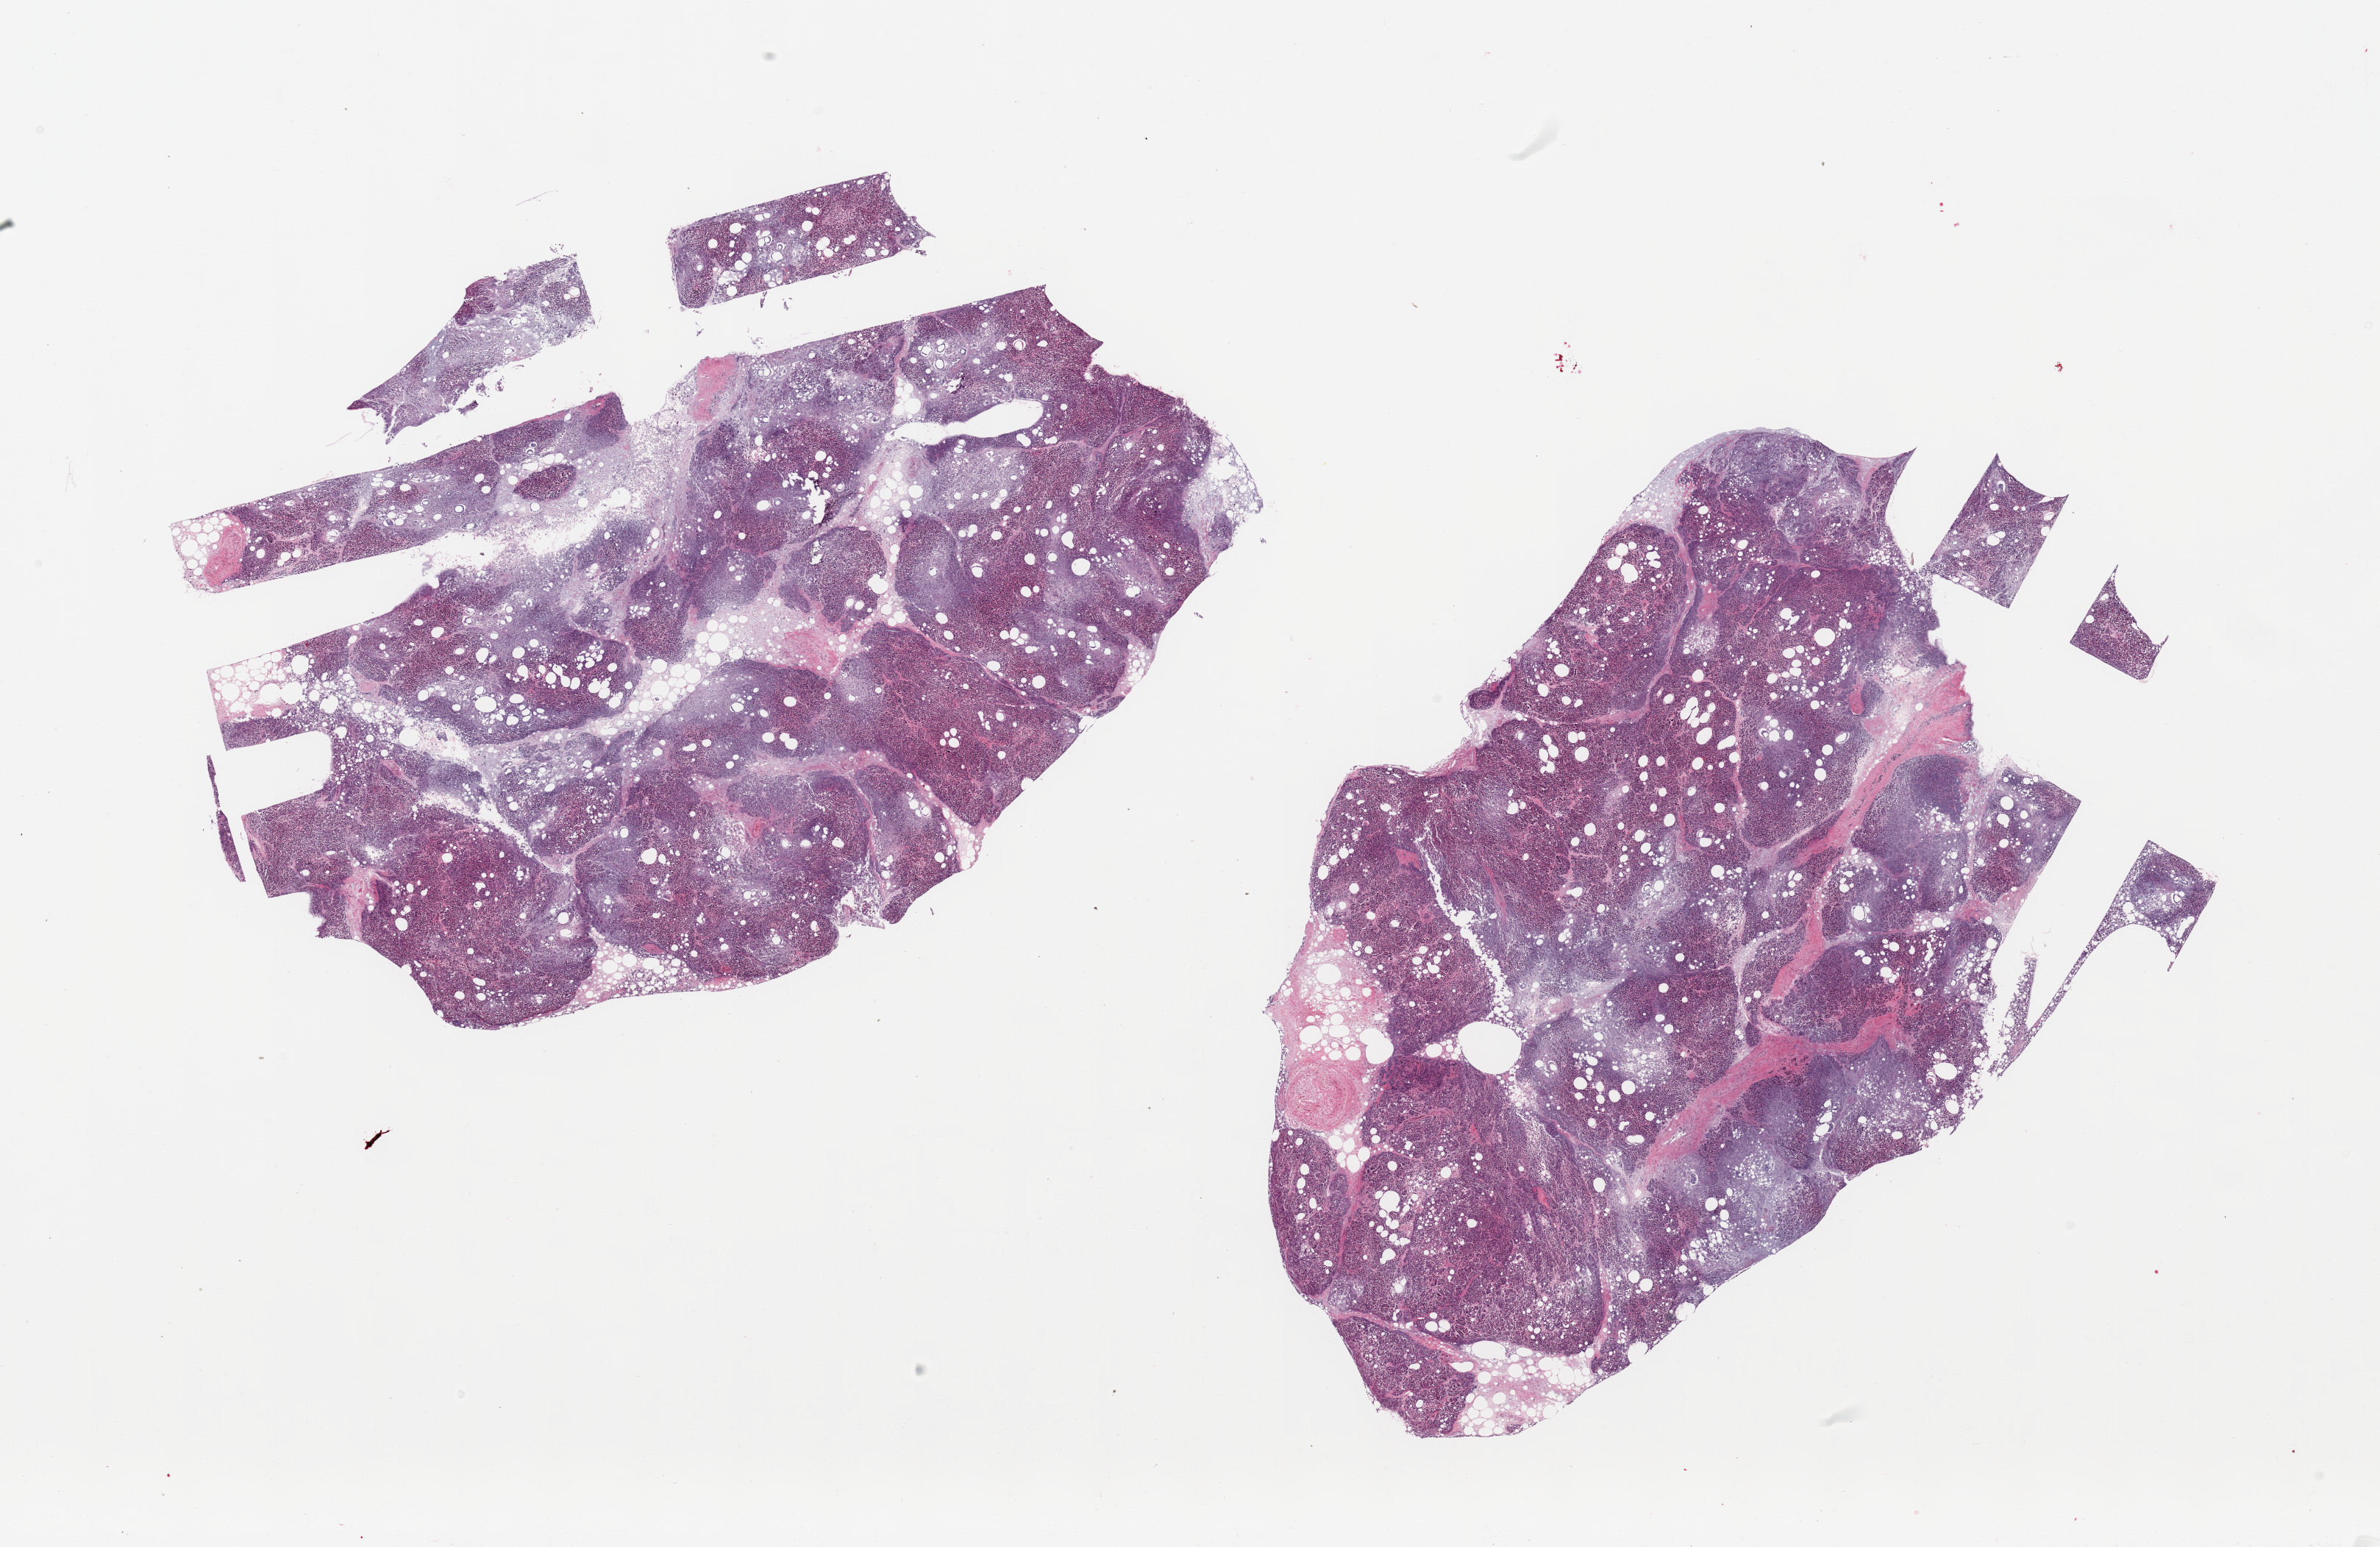
Whole-slide image, H&E stain, shown as a low-resolution overview of the whole scanned area (about 25.6 x 16.6 mm, acquisition: 20x scan), PAXgene-fixed paraffin-embedded (PFPE) section, section of pancreas (target tissue), donor tissue sample. Male donor.
Review note (as recorded): 2 pieces, advanced saponification, islets not visible.